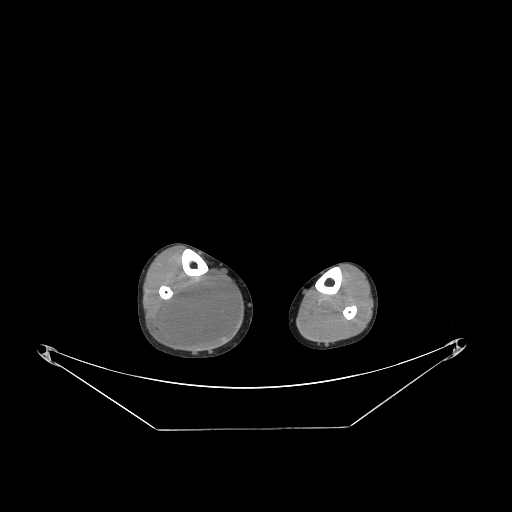
CT of an extremity soft-tissue mass (from a PET/CT study), one axial slice. Position 90 of 267 along the scan axis. Reconstruction kernel STANDARD. Soft-tissue window (W 400 / L 40 HU). 512 × 512 image matrix, field of view 500 × 500 mm. Male patient. From the clinical record (not read from this slice): histological type: liposarcoma - round cell; grade: high; site of the primary tumour: right calf.
Structures marked on this image (expert contour drawn on MRI and transferred to this co-registered scan by the dataset authors):
- gross tumour volume (mass): bounding box <155,274,239,348> (left, top, right, bottom; pixels)